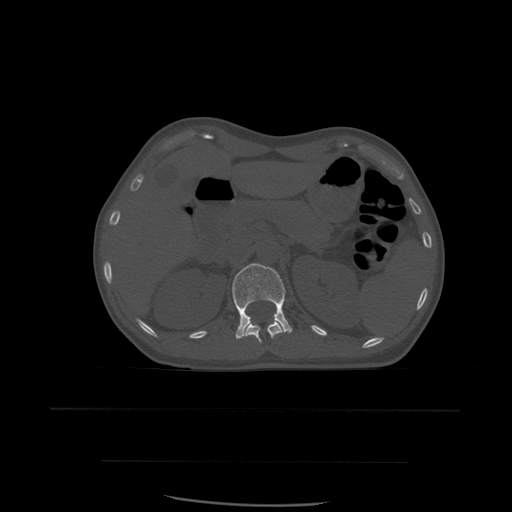
CT including the spine, one axial slice; slice 259 of 574 in the series (ordered by position); bone window (W 1800 / L 400 HU); 1.25 mm slice thickness; 512 × 512 image matrix, field of view 392 × 392 mm. Patient age 48 years. Case-level facts recorded for this patient, not image findings: primary cancer: lung; vertebrae with lytic lesions (as recorded): T11.
Structures marked on this image (semi-automatically segmented with operator editing):
- L1 vertebra: bounding box (x1, y1, x2, y2) in pixels: (232, 263, 293, 339)
- T12 vertebra: (245, 322, 284, 344)